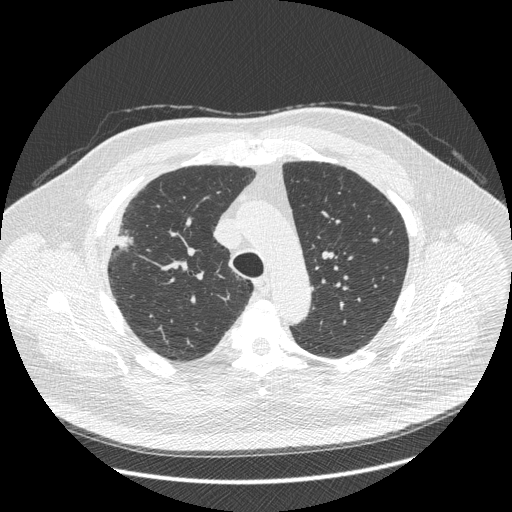
Low-dose screening chest CT, one axial slice; slice 314 of 426 in the series (ordered by position); 120 kVp; lung window (W 1500 / L -600 HU); 1.25 mm slice thickness; 512 × 512 image matrix, field of view 400 × 400 mm.
Annotated regions visible in this slice (manually delineated by an expert):
- lesion 1 (tumor, upper lobe of right lung): bounding box (x1, y1, x2, y2) in pixels: (117, 235, 130, 248)